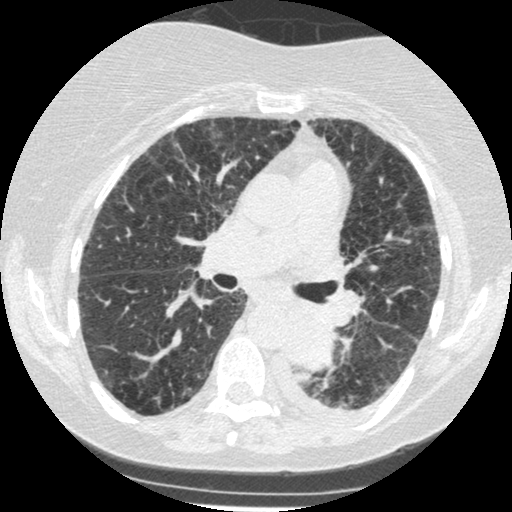
Low-dose screening chest CT, axial slice, third annual screen, lung window (W 1500 / L -600 HU), standard (soft-tissue) reconstruction kernel (STANDARD), slice 197 of 341 in the series, 512 × 512 image matrix. Female participant, aged 60 years at enrolment. Former smoker at enrolment.
Expert-annotated lung lesion, bounding box <270,307,341,374> (left, top, right, bottom; pixels). Screening reader's record for this exam (one nodule recorded; not confirmed to be the boxed lesion): non-calcified nodule or mass ≥4 mm, left lower lobe, 54 × 38 mm, smooth margins, soft tissue attenuation, pre-existing on the prior screen: yes; interval growth: yes.